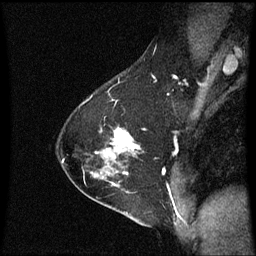
Breast MRI (dynamic contrast-enhanced), one sagittal slice; position 41 of 60 along the scan axis; dynamic contrast-enhanced series, image 2 of 3 at this slice position (ordered by acquisition); 1.5 T; TE 4.2 ms, TR 8.9 ms; 2 mm slice thickness; 256 × 256 image matrix. Patient: female, 54 years. Case-level facts recorded for this patient, not image findings: setting: breast cancer imaged before/during neoadjuvant chemotherapy; receptor status: HER2-positive.
Outlined on this slice (semi-automatically segmented with operator editing):
- analysis volume of interest (the breast-tissue region the enhancement analysis was run in; not a lesion): box from (x=102, y=126) to (x=141, y=169) px
- tumour enhancement mask (voxels above the 70 % enhancement threshold inside the analysis volume of interest): (x=113, y=128)–(x=138, y=151)